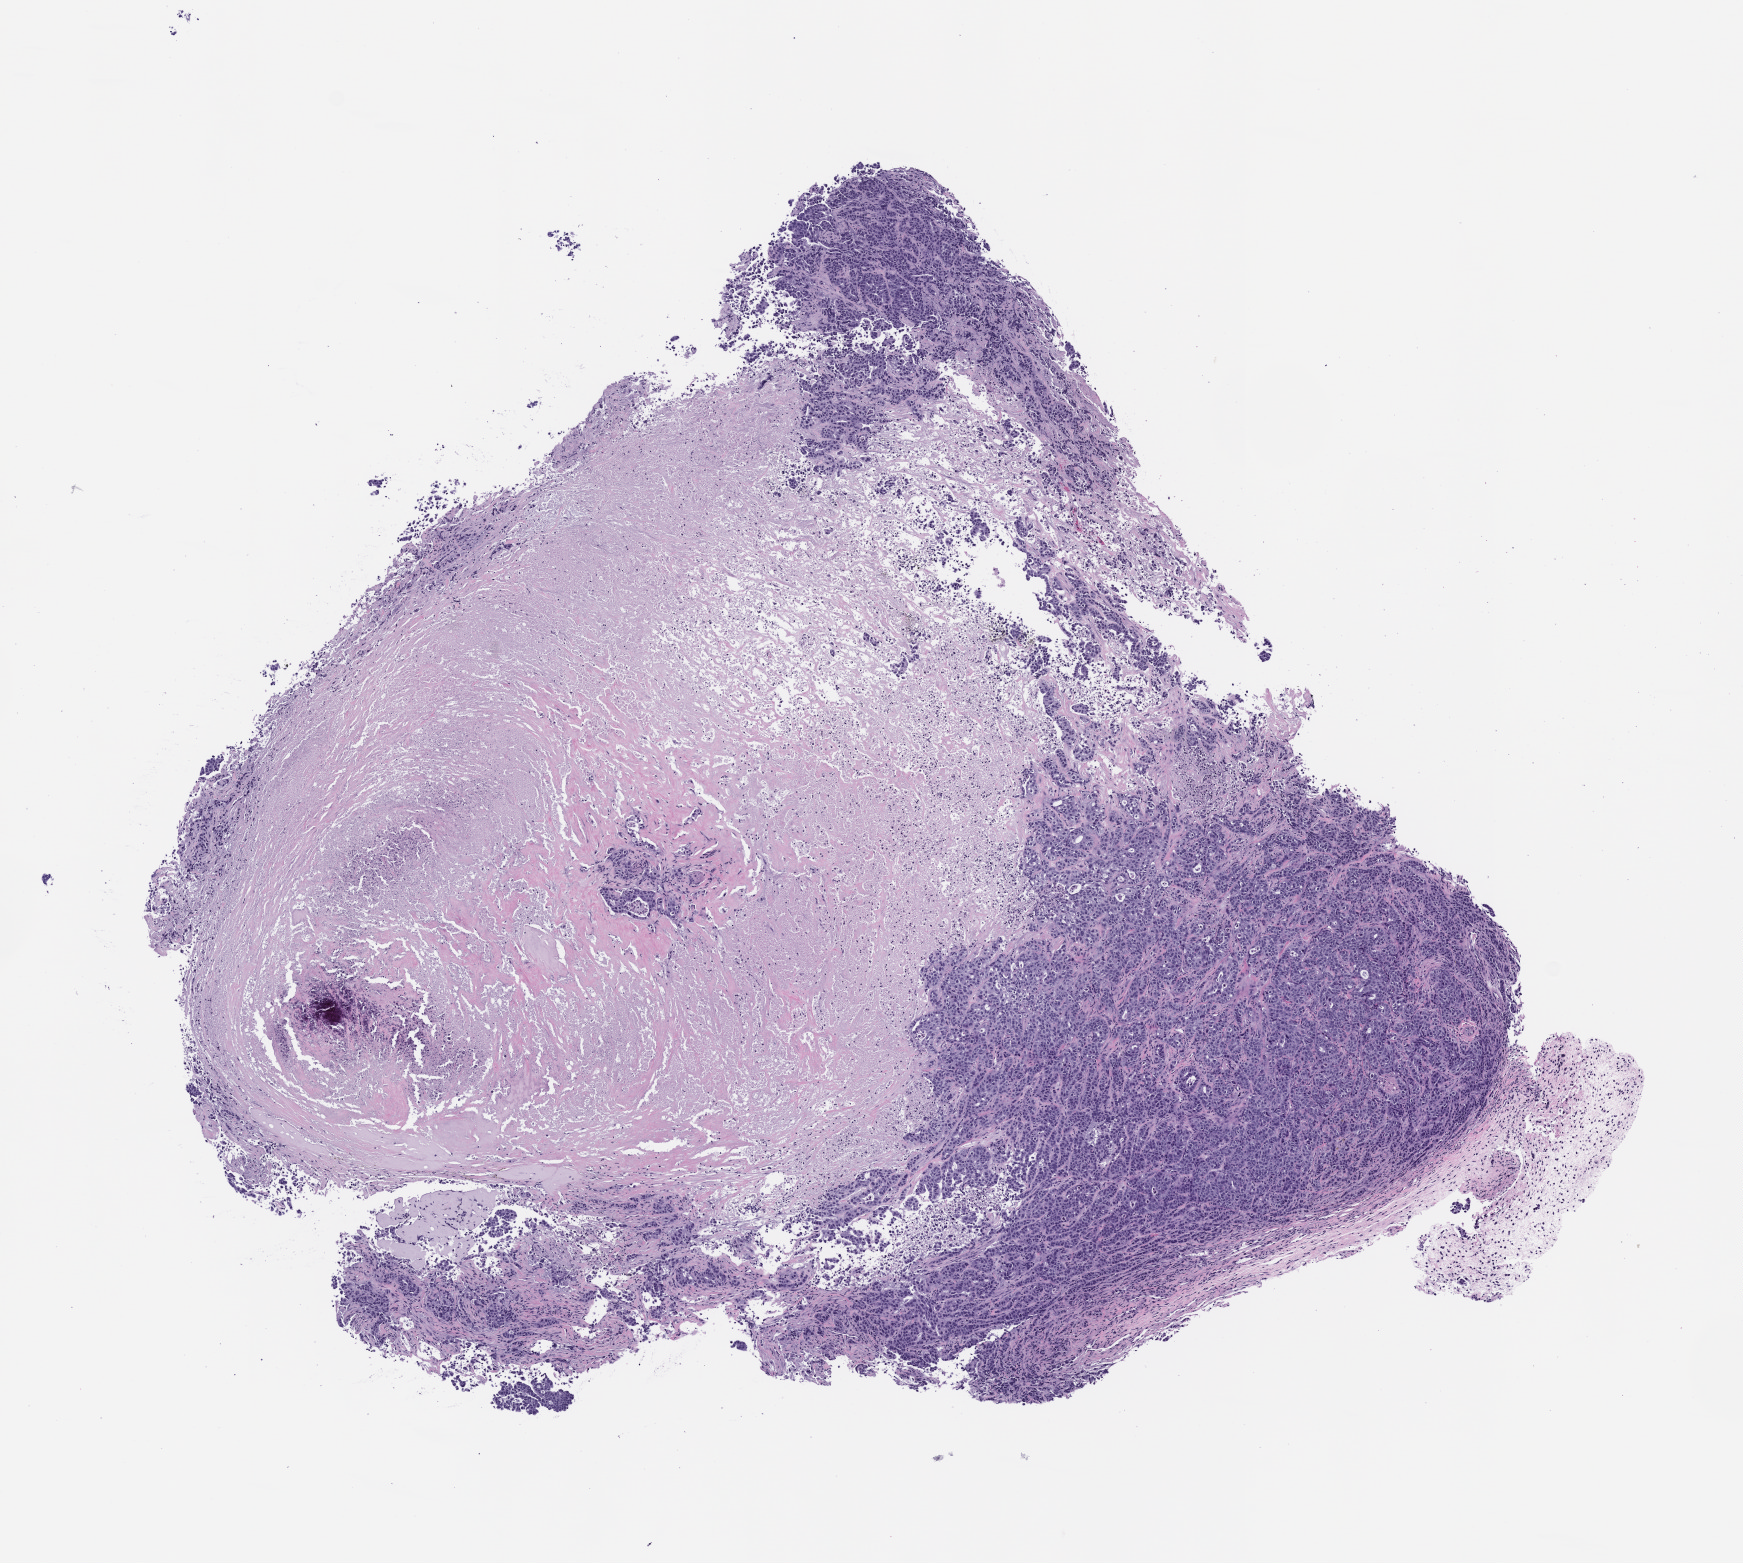
Haematoxylin and eosin whole-slide image of a patient-derived xenograft (PDX) tumor grown in a mouse — a low-resolution overview of the entire scanned area, about 7.0 x 6.3 mm; formalin-fixed, paraffin-embedded (FFPE) tissue; tumor site category: lung.
Originating patient diagnosis: Lung Adenocarcinoma.